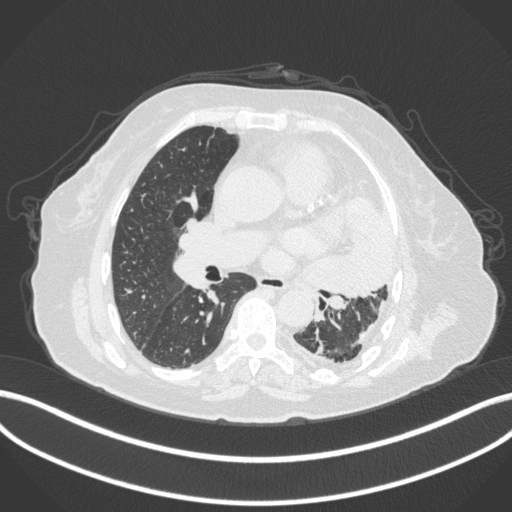
Chest CT, one axial slice; slice 195 of 399 in the series (ordered by position); reconstruction kernel B31f; 120 kVp; lung window (W 1500 / L -600 HU); 1 mm slice thickness; 512 × 512 image matrix, field of view 400 × 400 mm. Female patient, age 75 years. Case-level facts recorded for this patient, not image findings: clinical TNM (as recorded): T3 N3 M1.
Outlined on this slice (rectangle marked by the reading radiologist):
- lung tumour (recorded histology: adenocarcinoma): bounding box (x1, y1, x2, y2) in pixels: (297, 188, 401, 305)